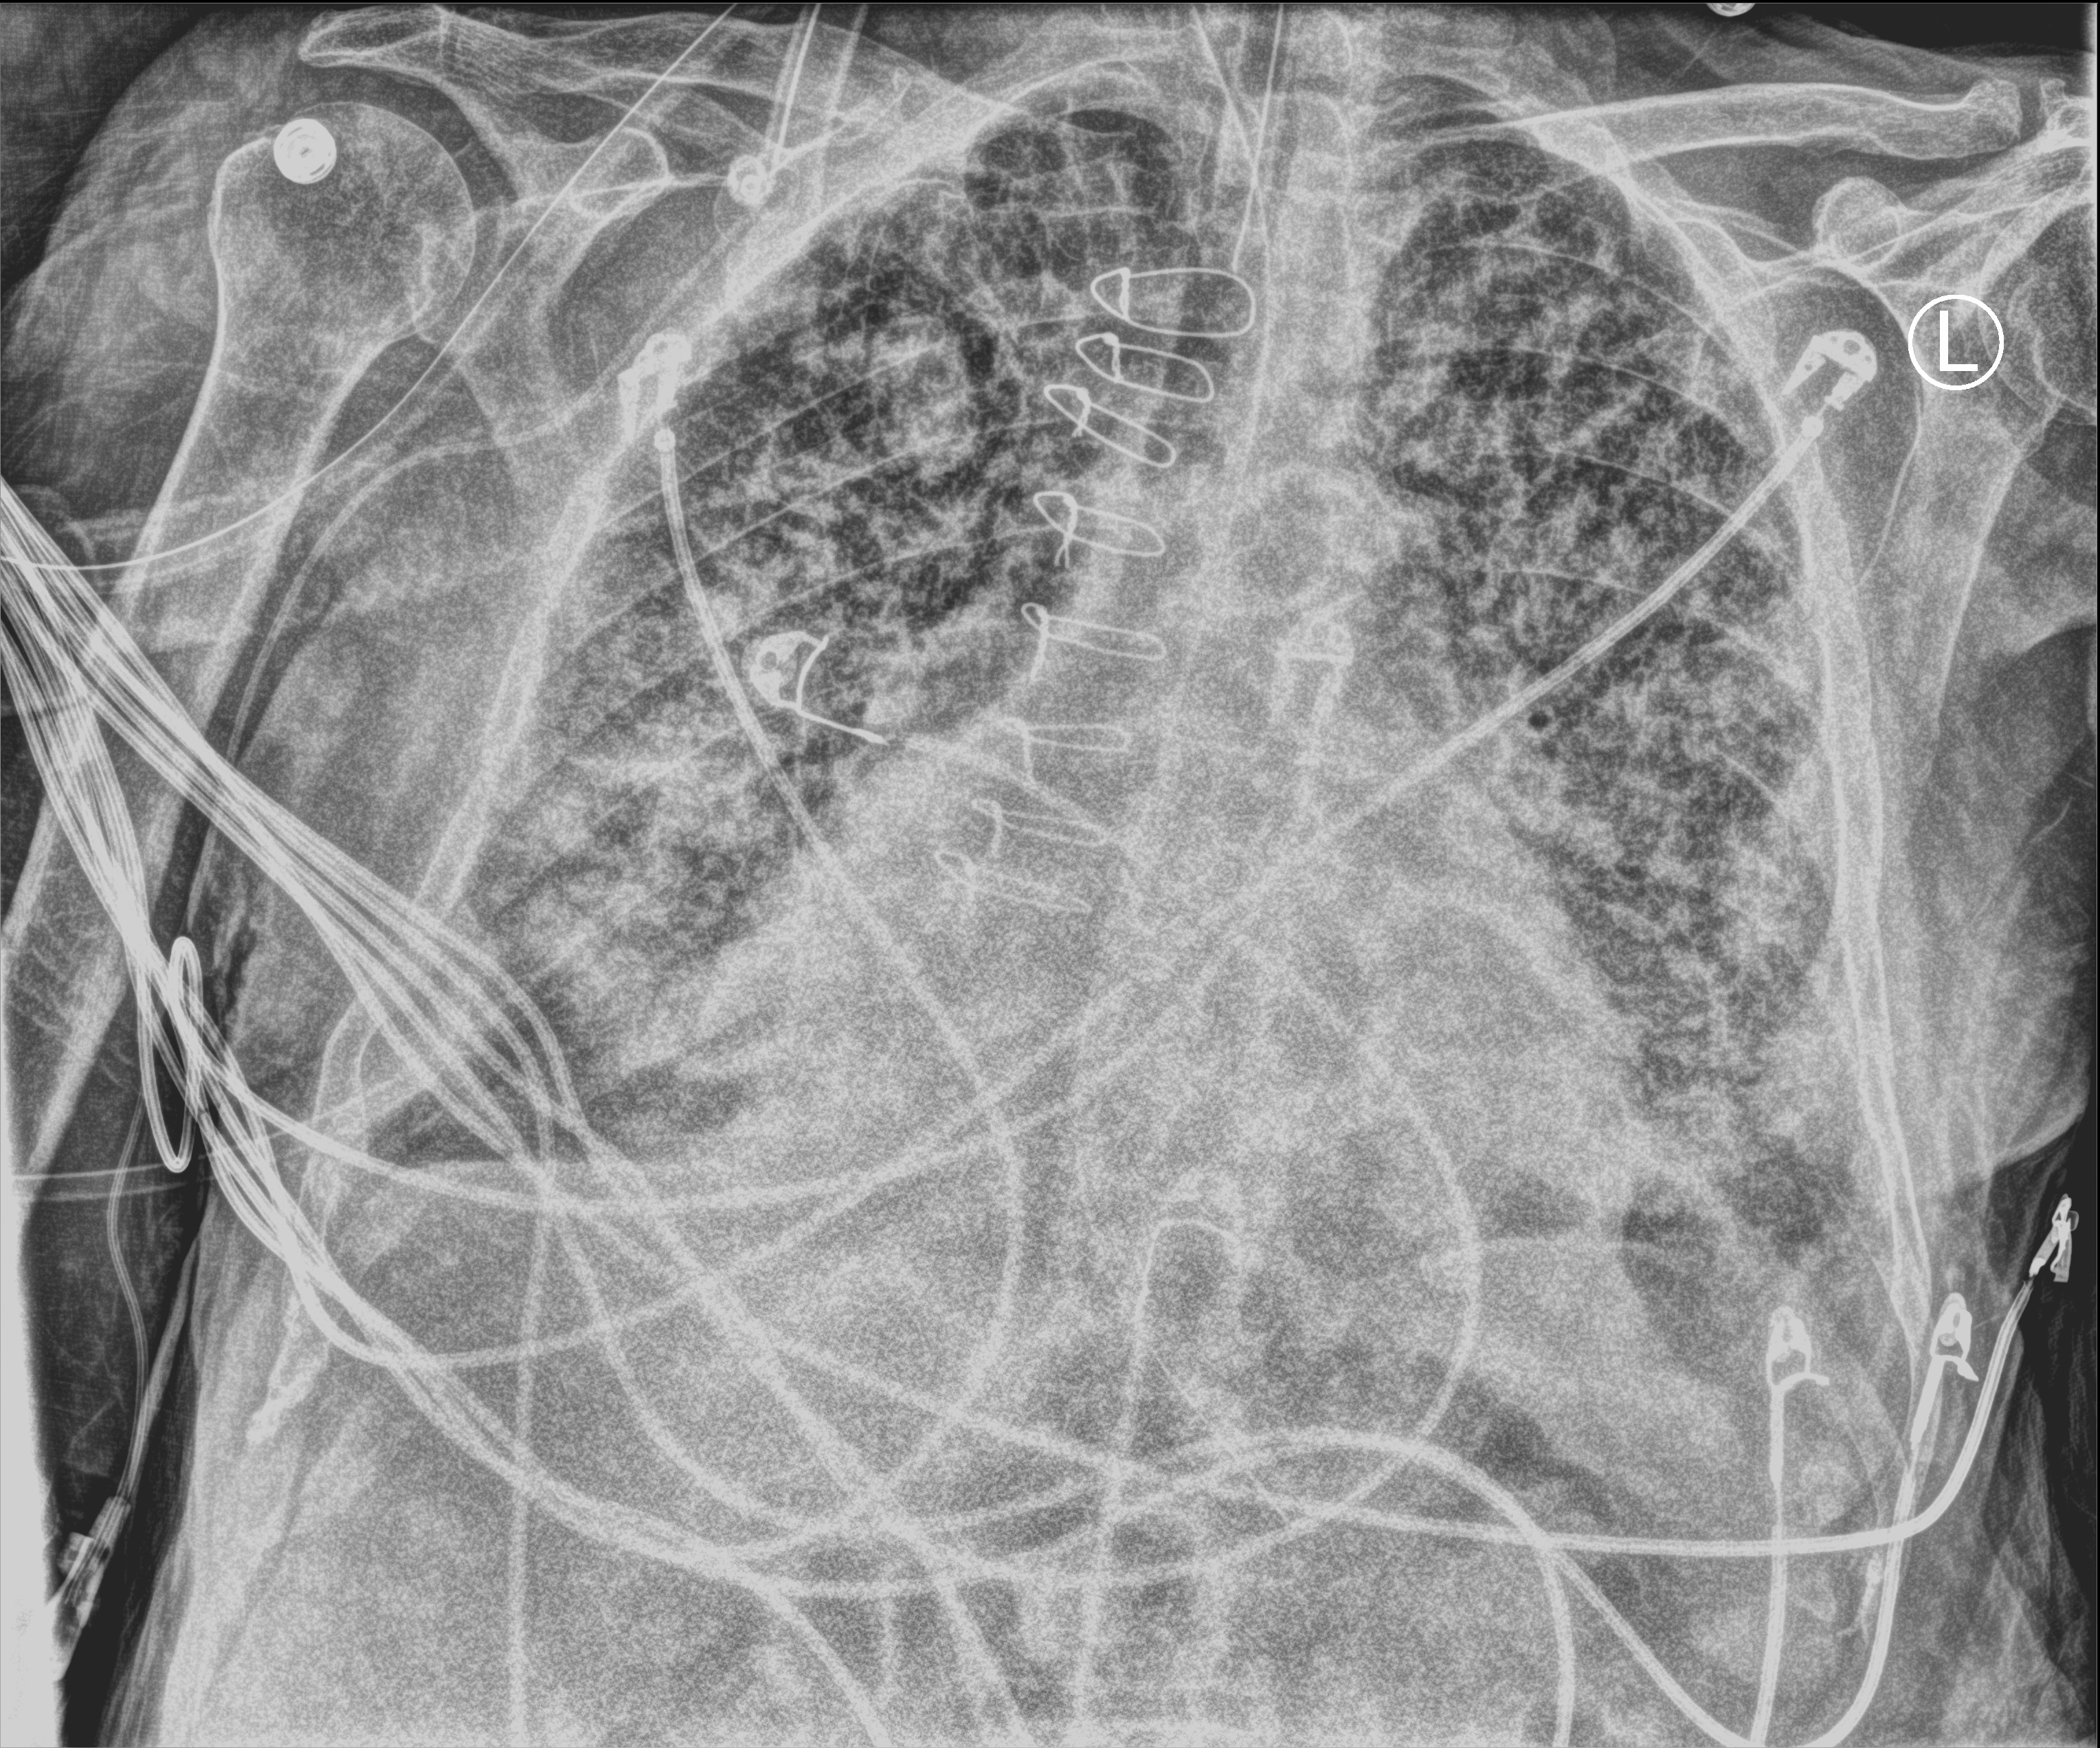
Chest X-ray (portable). Male patient hospitalised with COVID-19, age 75–90 years.
Admission-level facts for this patient (not findings on this image; timing relative to this image not recorded): admitted to intensive care during this hospital stay: yes.